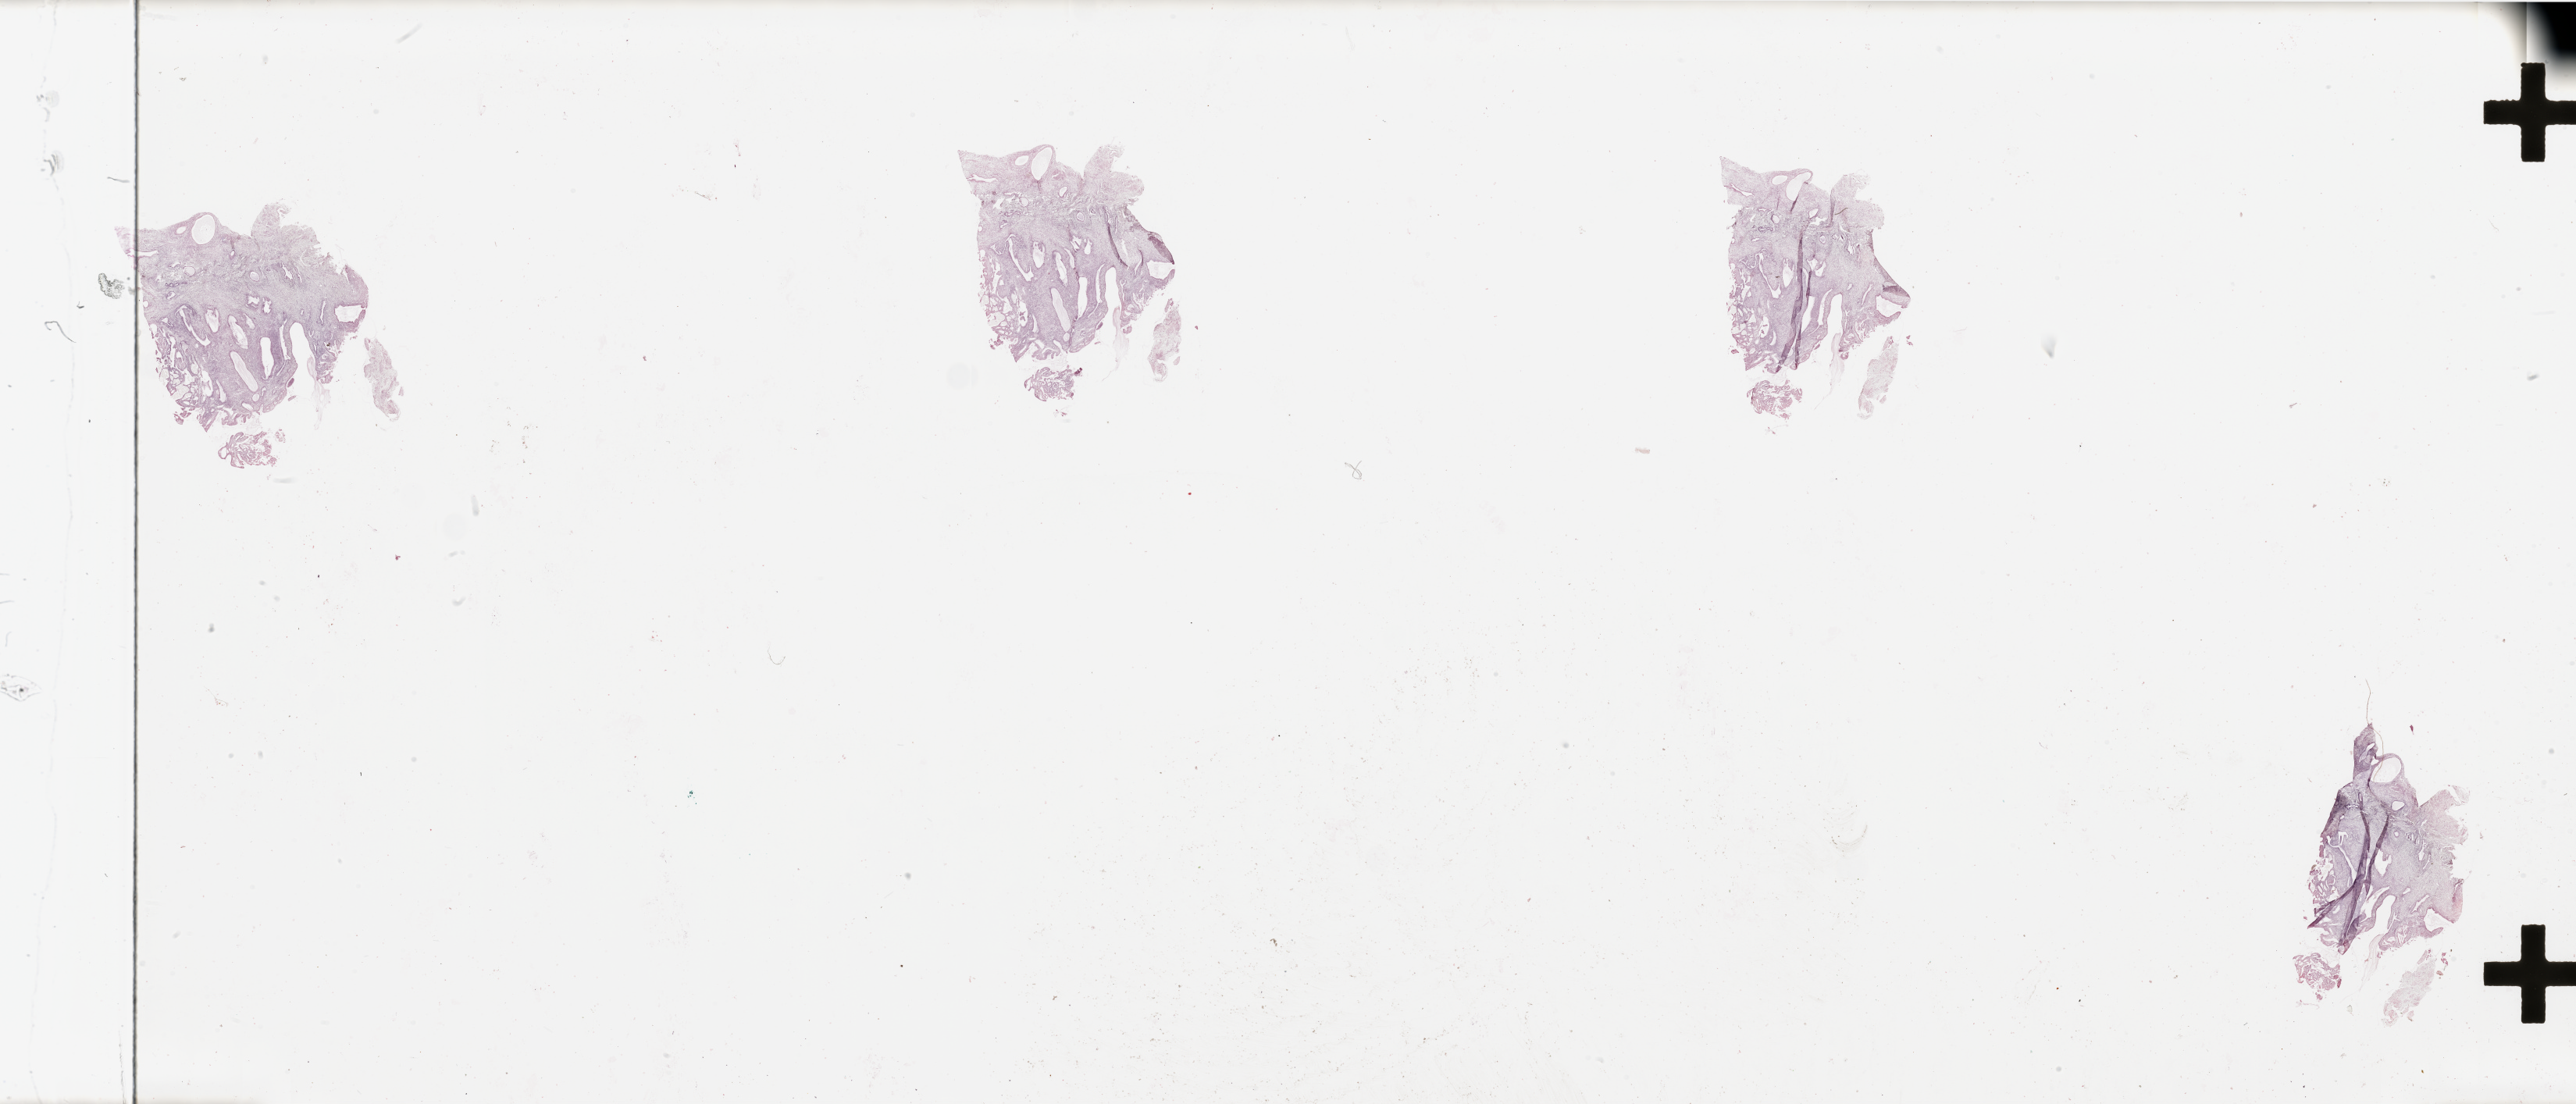
Whole-slide histology image, Hematoxylin and eosin (H&E) stained — a low-resolution overview of the entire scanned area, about 52.2 x 22.4 mm, normal (non-tumour) tissue sample, sampled site: uterus. Patient: female, age 58 years.
- this section: normal (non-tumour) tissue from the same patient
- patient diagnosis: Endometrioid adenocarcinoma, NOS